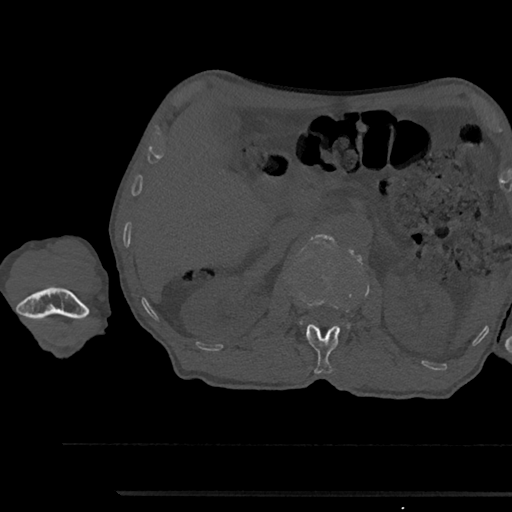
CT including the spine, one axial slice. Slice 613 of 797 in the series (ordered by position). Reconstruction kernel Br40s/3. Bone window (W 1800 / L 400 HU). 0.5 mm slice thickness. 512 × 512 image matrix. Patient: male, 79 years. Case-level facts recorded for this patient, not image findings: primary cancer: prostate.
Outlined on this slice (semi-automatically segmented with operator editing):
- L1 vertebra: bounding box [x1, y1, x2, y2] px = [296, 297, 340, 374]
- L2 vertebra: [301, 234, 349, 326]